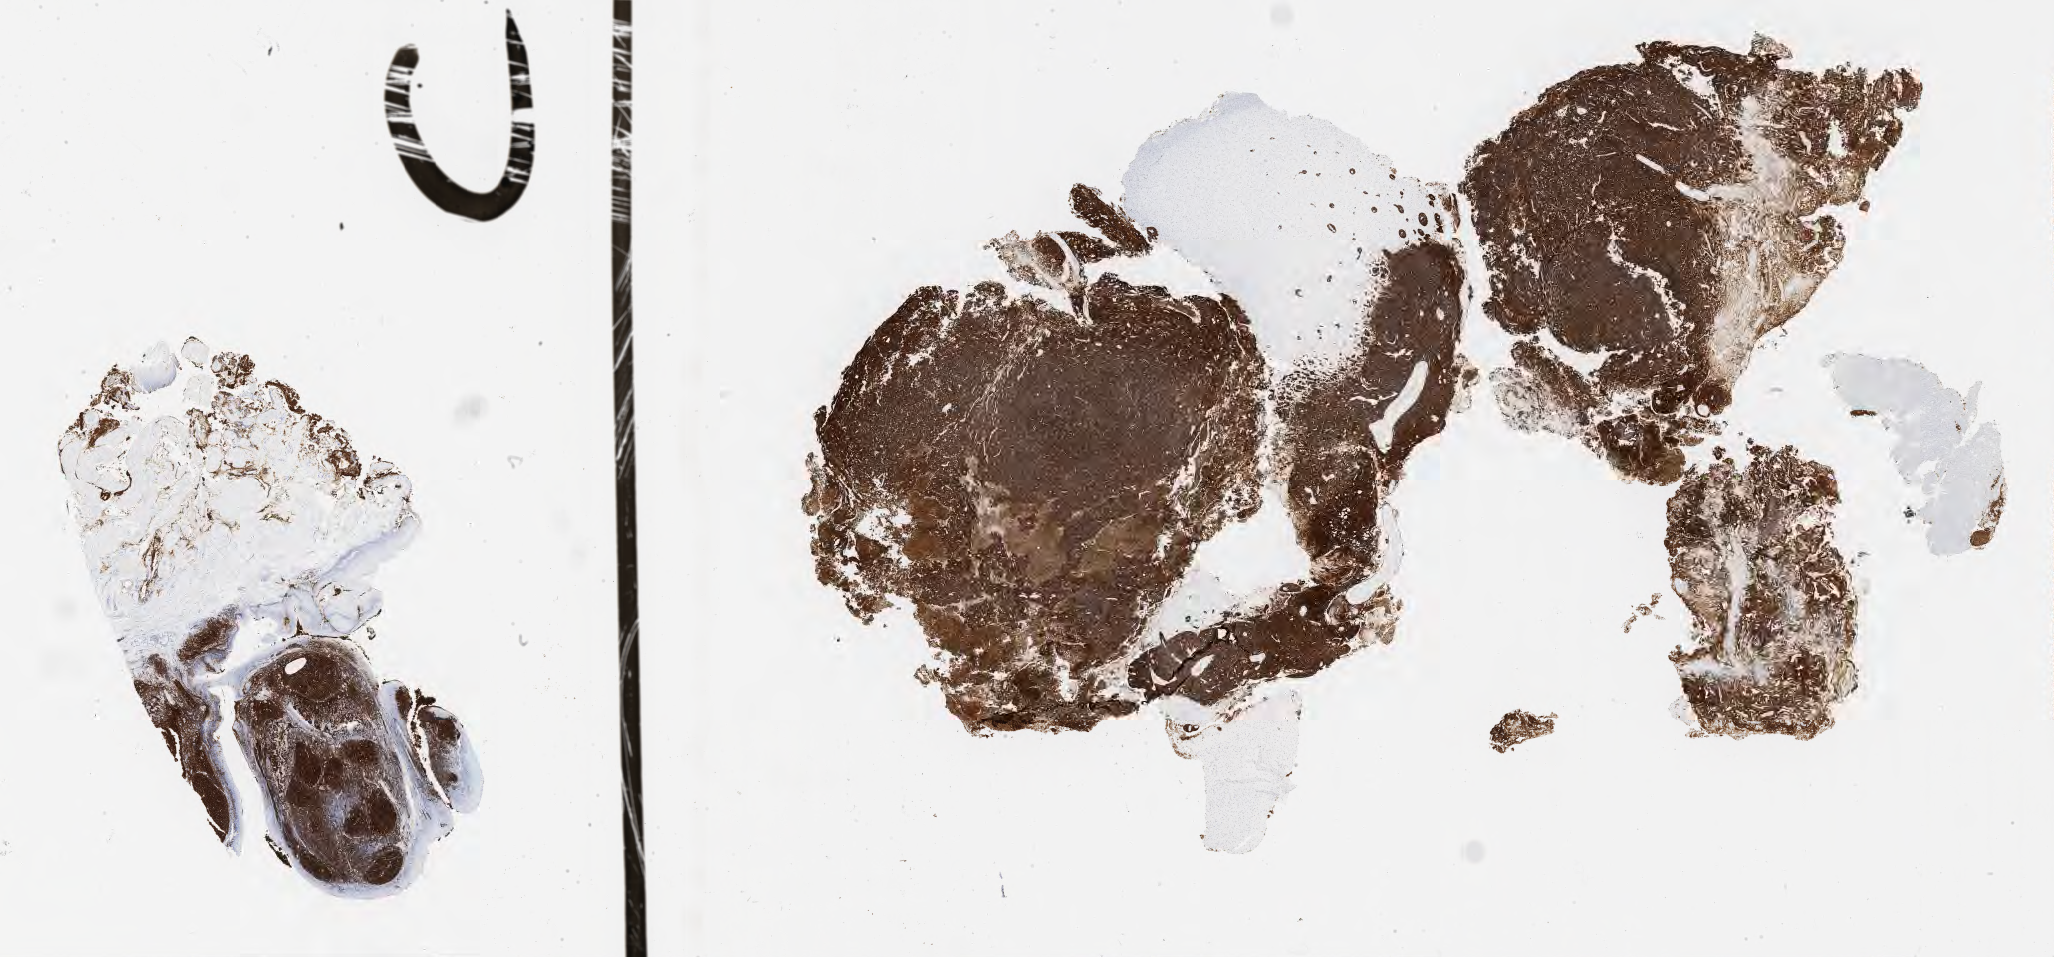
Immunohistochemistry (IHC) whole-slide image stained for CD20 — low-resolution overview of the scanned area, about 33.2 x 15.5 mm, tumor tissue. Patient female; aged 73.
- diagnosis: Burkitt lymphoma, NOS